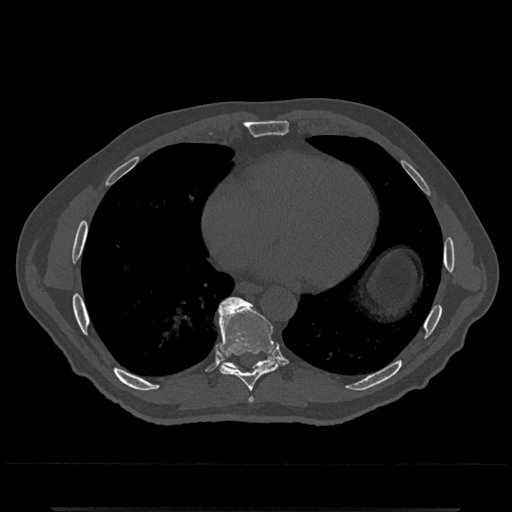
CT including the spine, one axial slice. Slice 653 of 797 in the series (ordered by position). Reconstruction kernel Br40s/3. Bone window (W 1800 / L 400 HU). 0.5 mm slice thickness. 512 × 512 image matrix. Patient: male, 67 years. Case-level facts recorded for this patient, not image findings: primary cancer: prostate.
Annotated regions visible in this slice (semi-automatic segmentation, software-assisted and operator-edited):
- T7 vertebra: bounding box <249,397,254,402> (left, top, right, bottom; pixels)
- T8 vertebra: <217,297,280,391>
- T9 vertebra: <217,297,278,371>